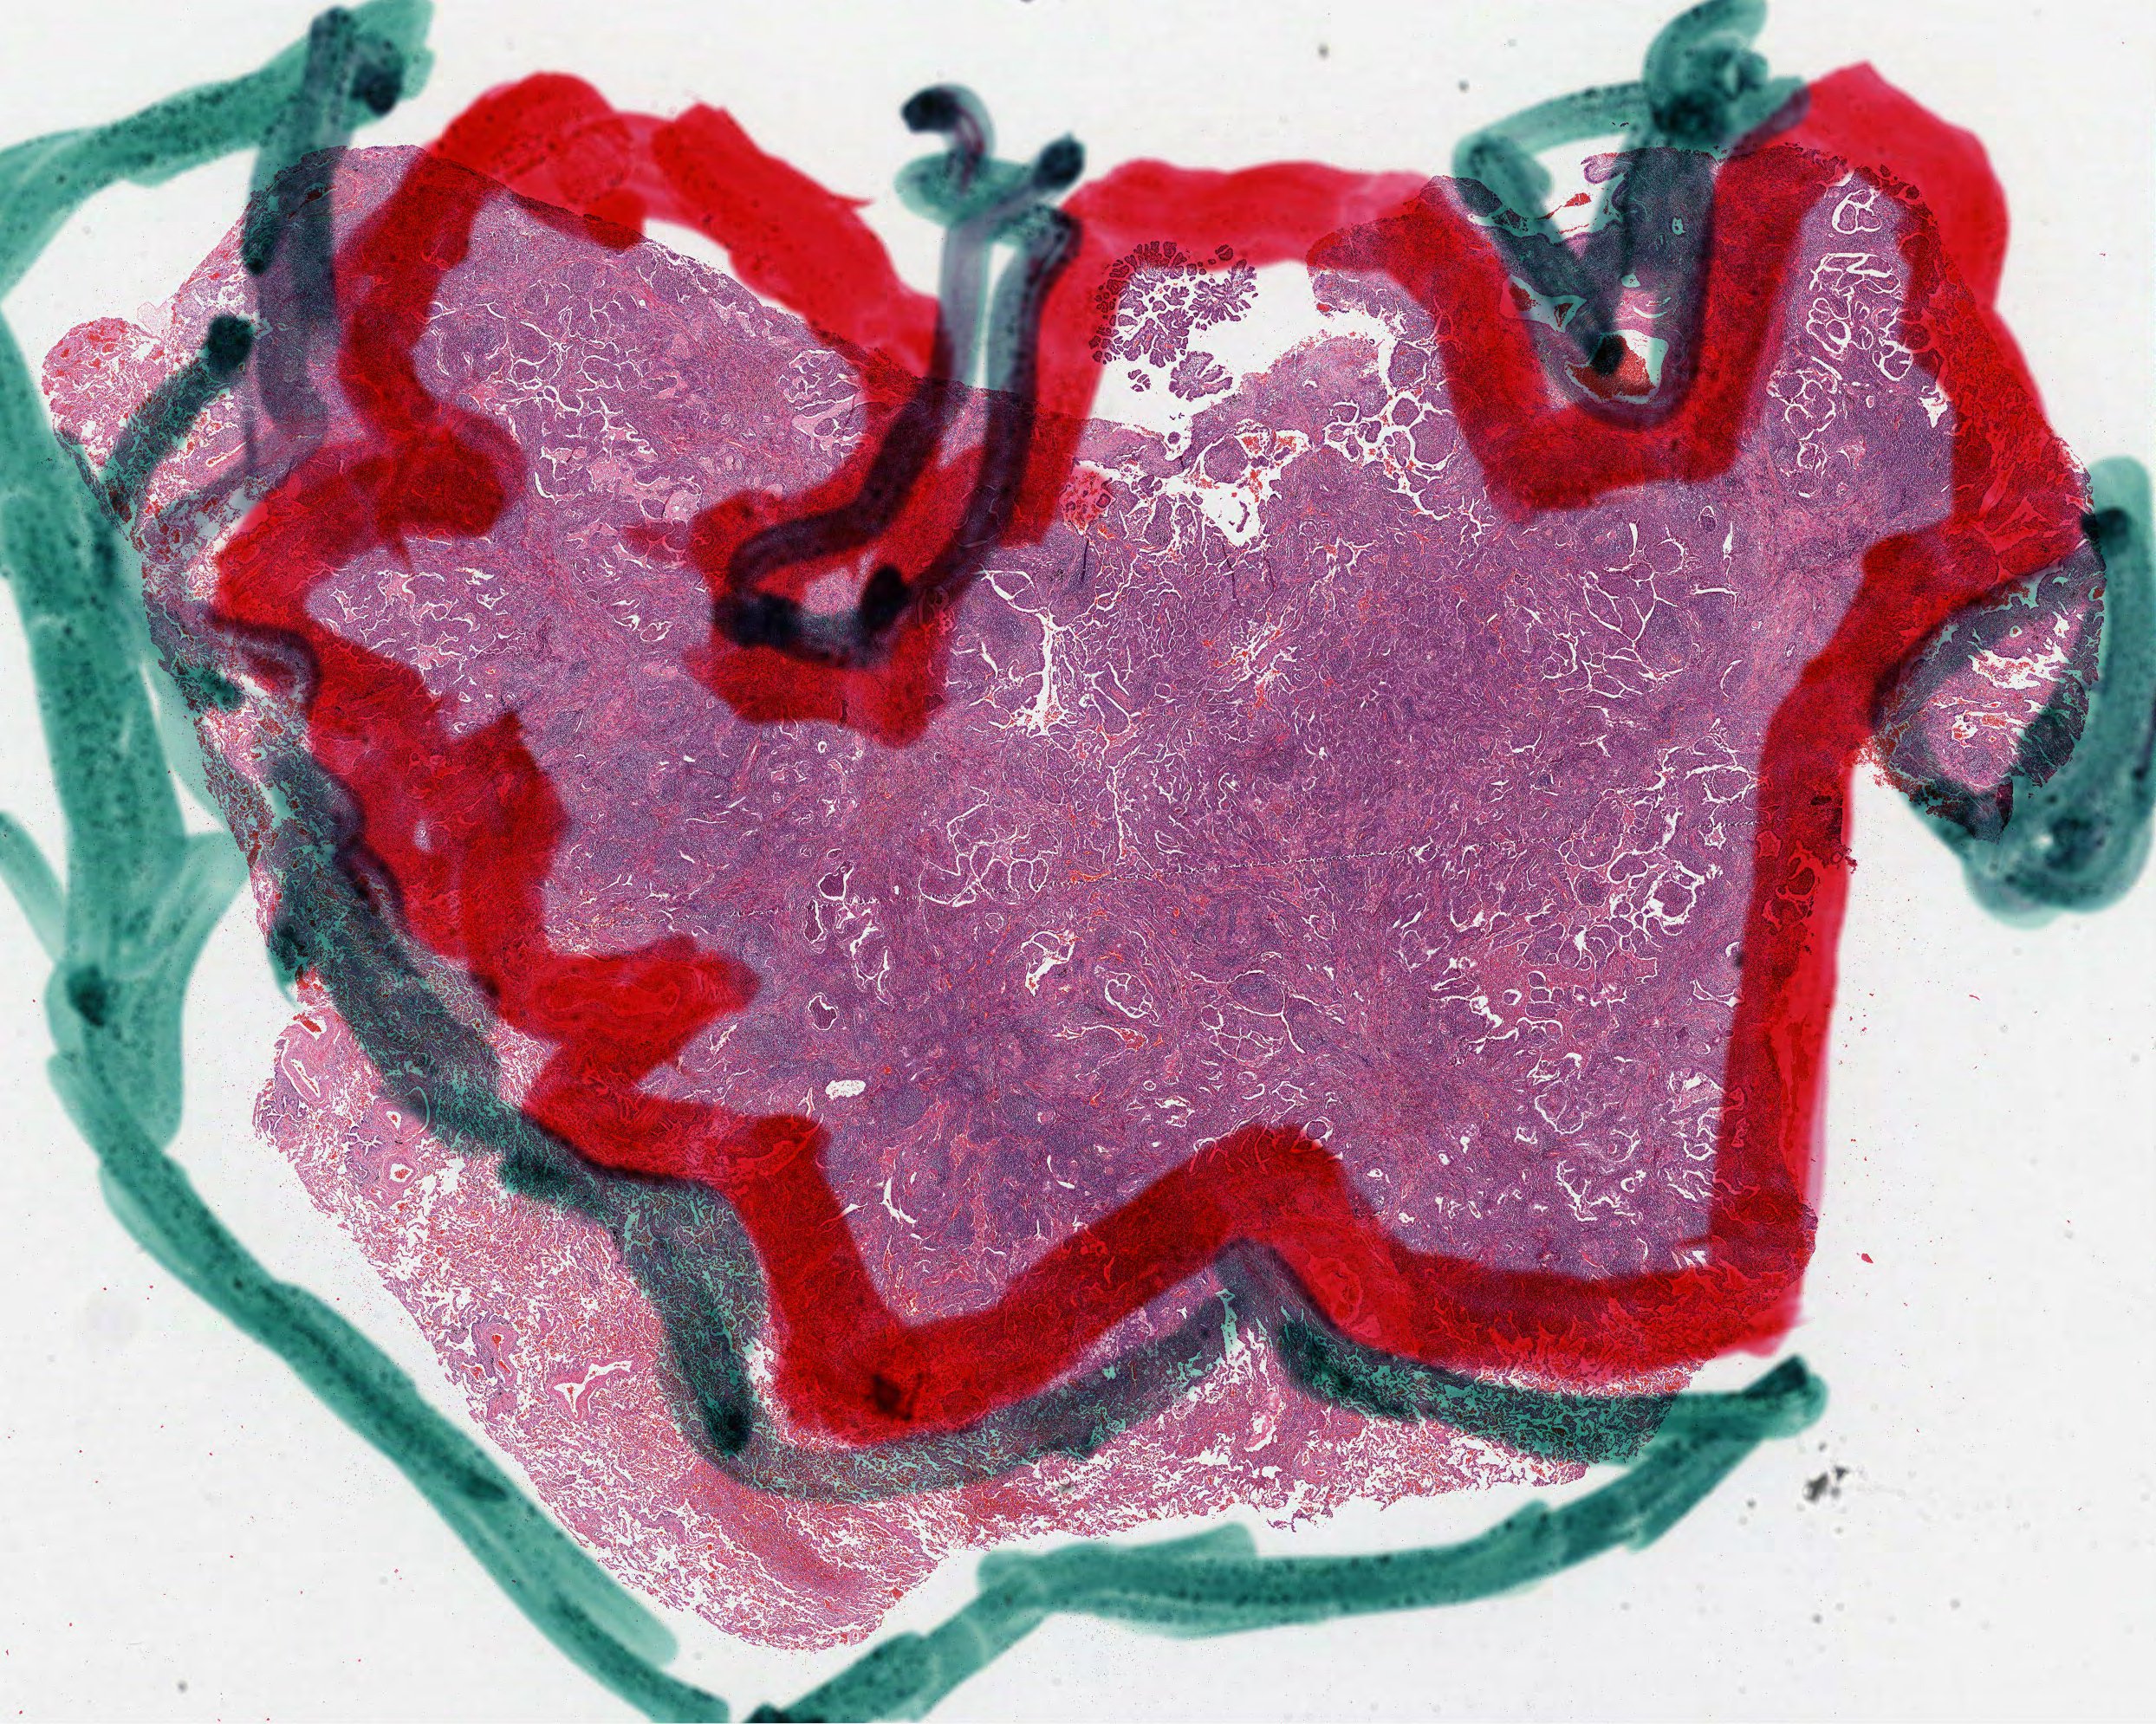
Whole-slide histology image, H&E-stained — whole scanned area (about 20.1 x 16.0 mm) shown as a low-resolution overview; formalin-fixed paraffin-embedded (FFPE) diagnostic section; lung, primary tumour sample. Patient: male, age at initial diagnosis 42 years.
Histologic diagnosis: Papillary adenocarcinoma, NOS (upper lobe, lung). TNM: T1 N0 M0. AJCC pathologic stage: IA (7th edition).